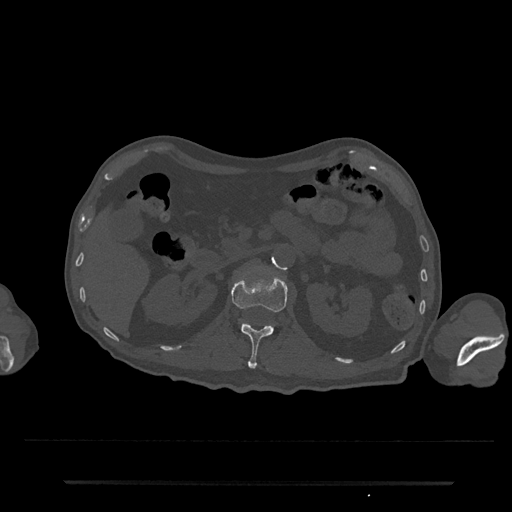
CT including the spine, one axial slice; position 115 of 797 along the scan axis; reconstruction kernel Br40s/3; bone window (W 1800 / L 400 HU); 512 × 512 image matrix, field of view 427 × 427 mm. Patient: male, 74 years. From the clinical record (not read from this slice): primary cancer: prostate.
Outlined on this slice (semi-automatically segmented with operator editing):
- L1 vertebra: bounding box (x1, y1, x2, y2) in pixels: (231, 268, 288, 369)